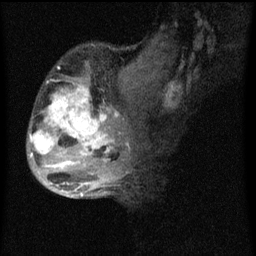
Breast MRI (dynamic contrast-enhanced), one sagittal slice; position 26 of 60 along the scan axis; dynamic contrast-enhanced series, image 2 of 4 at this slice position (ordered by acquisition); 1.5 T; TE 4.2 ms, TR 8 ms; 2 mm slice thickness; 256 × 256 image matrix. Female patient, age 50 years.
Structures marked on this image (semi-automatically segmented with operator editing):
- analysis volume of interest (the breast-tissue region the enhancement analysis was run in; not a lesion): bounding box <28,44,124,177> (left, top, right, bottom; pixels)
- tumour enhancement mask (voxels above the 70 % enhancement threshold inside the analysis volume of interest): <30,80,120,169>